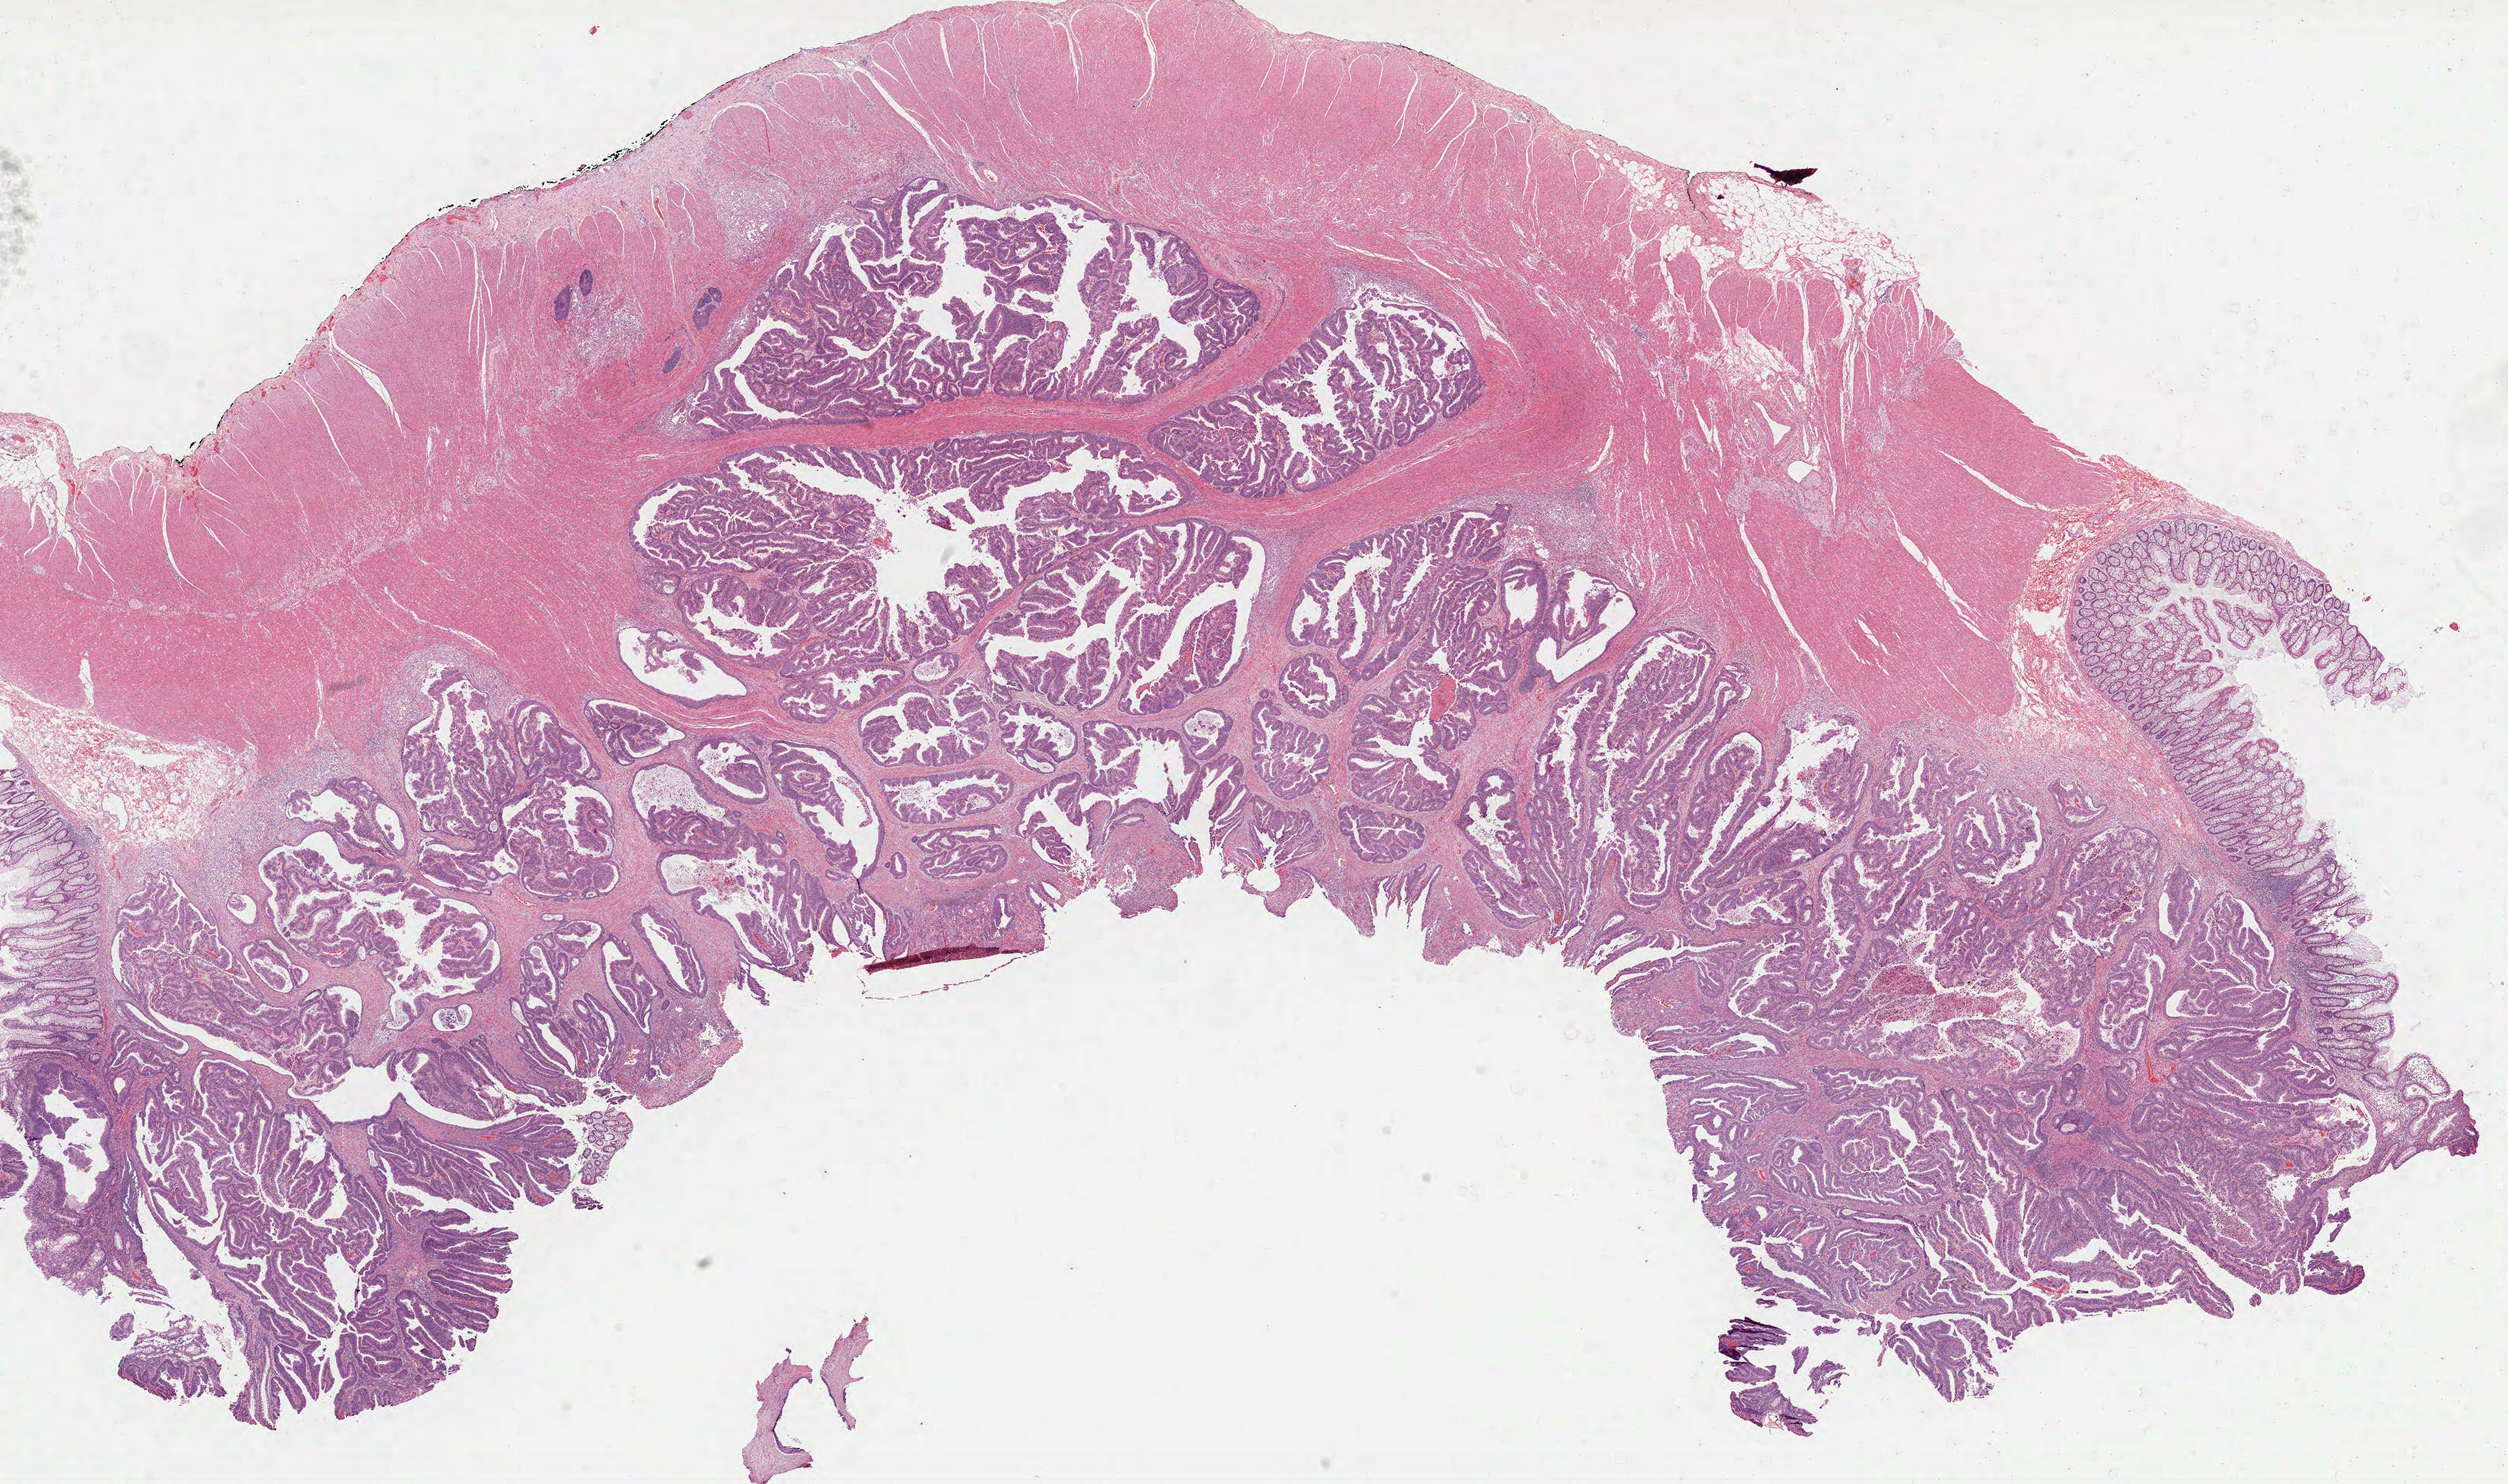
Hematoxylin and eosin (H&E) stained whole-slide image, a low-resolution overview of the entire scanned area, about 26.3 x 15.6 mm (from a 40x scan). FFPE section. Primary tumour sample from the colon. Female patient; age at initial diagnosis 37 years.
Pathologic diagnosis: Adenocarcinoma, NOS (sigmoid colon).